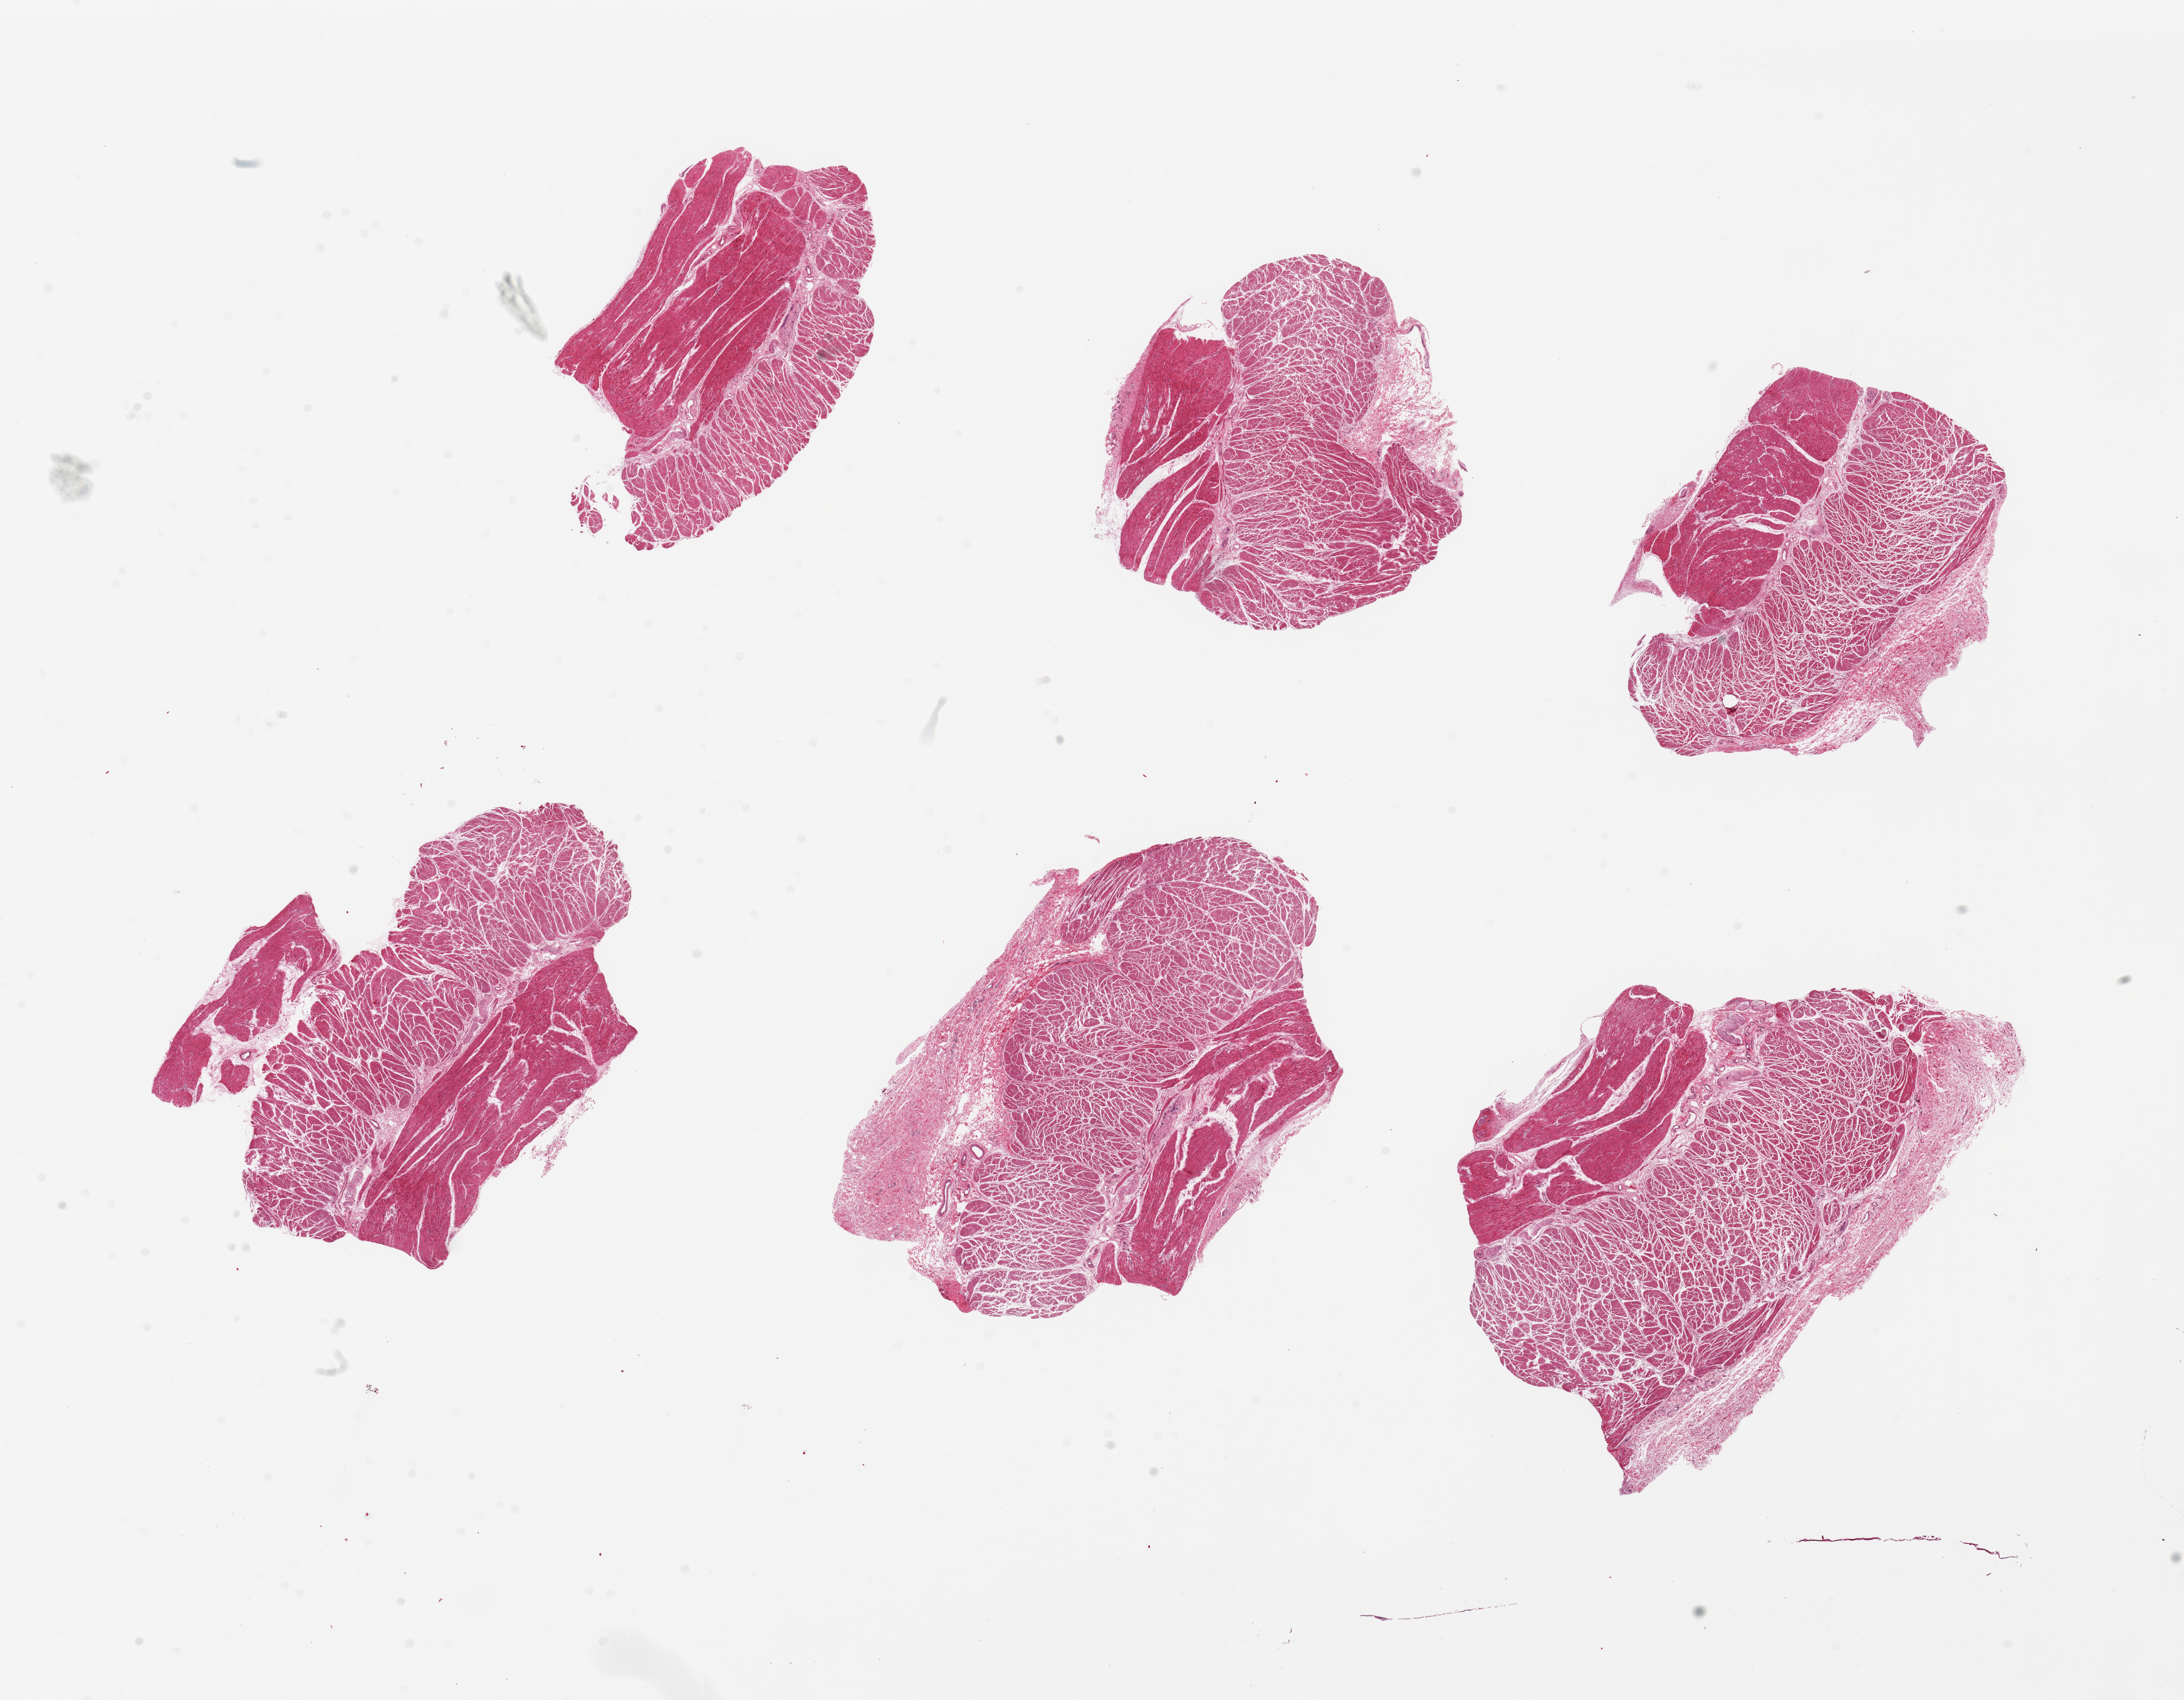
Whole-slide image, haematoxylin and eosin stain — shown as a low-resolution overview of the whole scanned area (about 27.6 x 21.5 mm), PAXgene-fixed paraffin-embedded (PFPE) section, sampled site (target tissue): esophageal muscle, tissue donor sample.
• reviewer comment on this tissue sample: 6 pieces, up to 8x5mm; all muscularis, good specimens